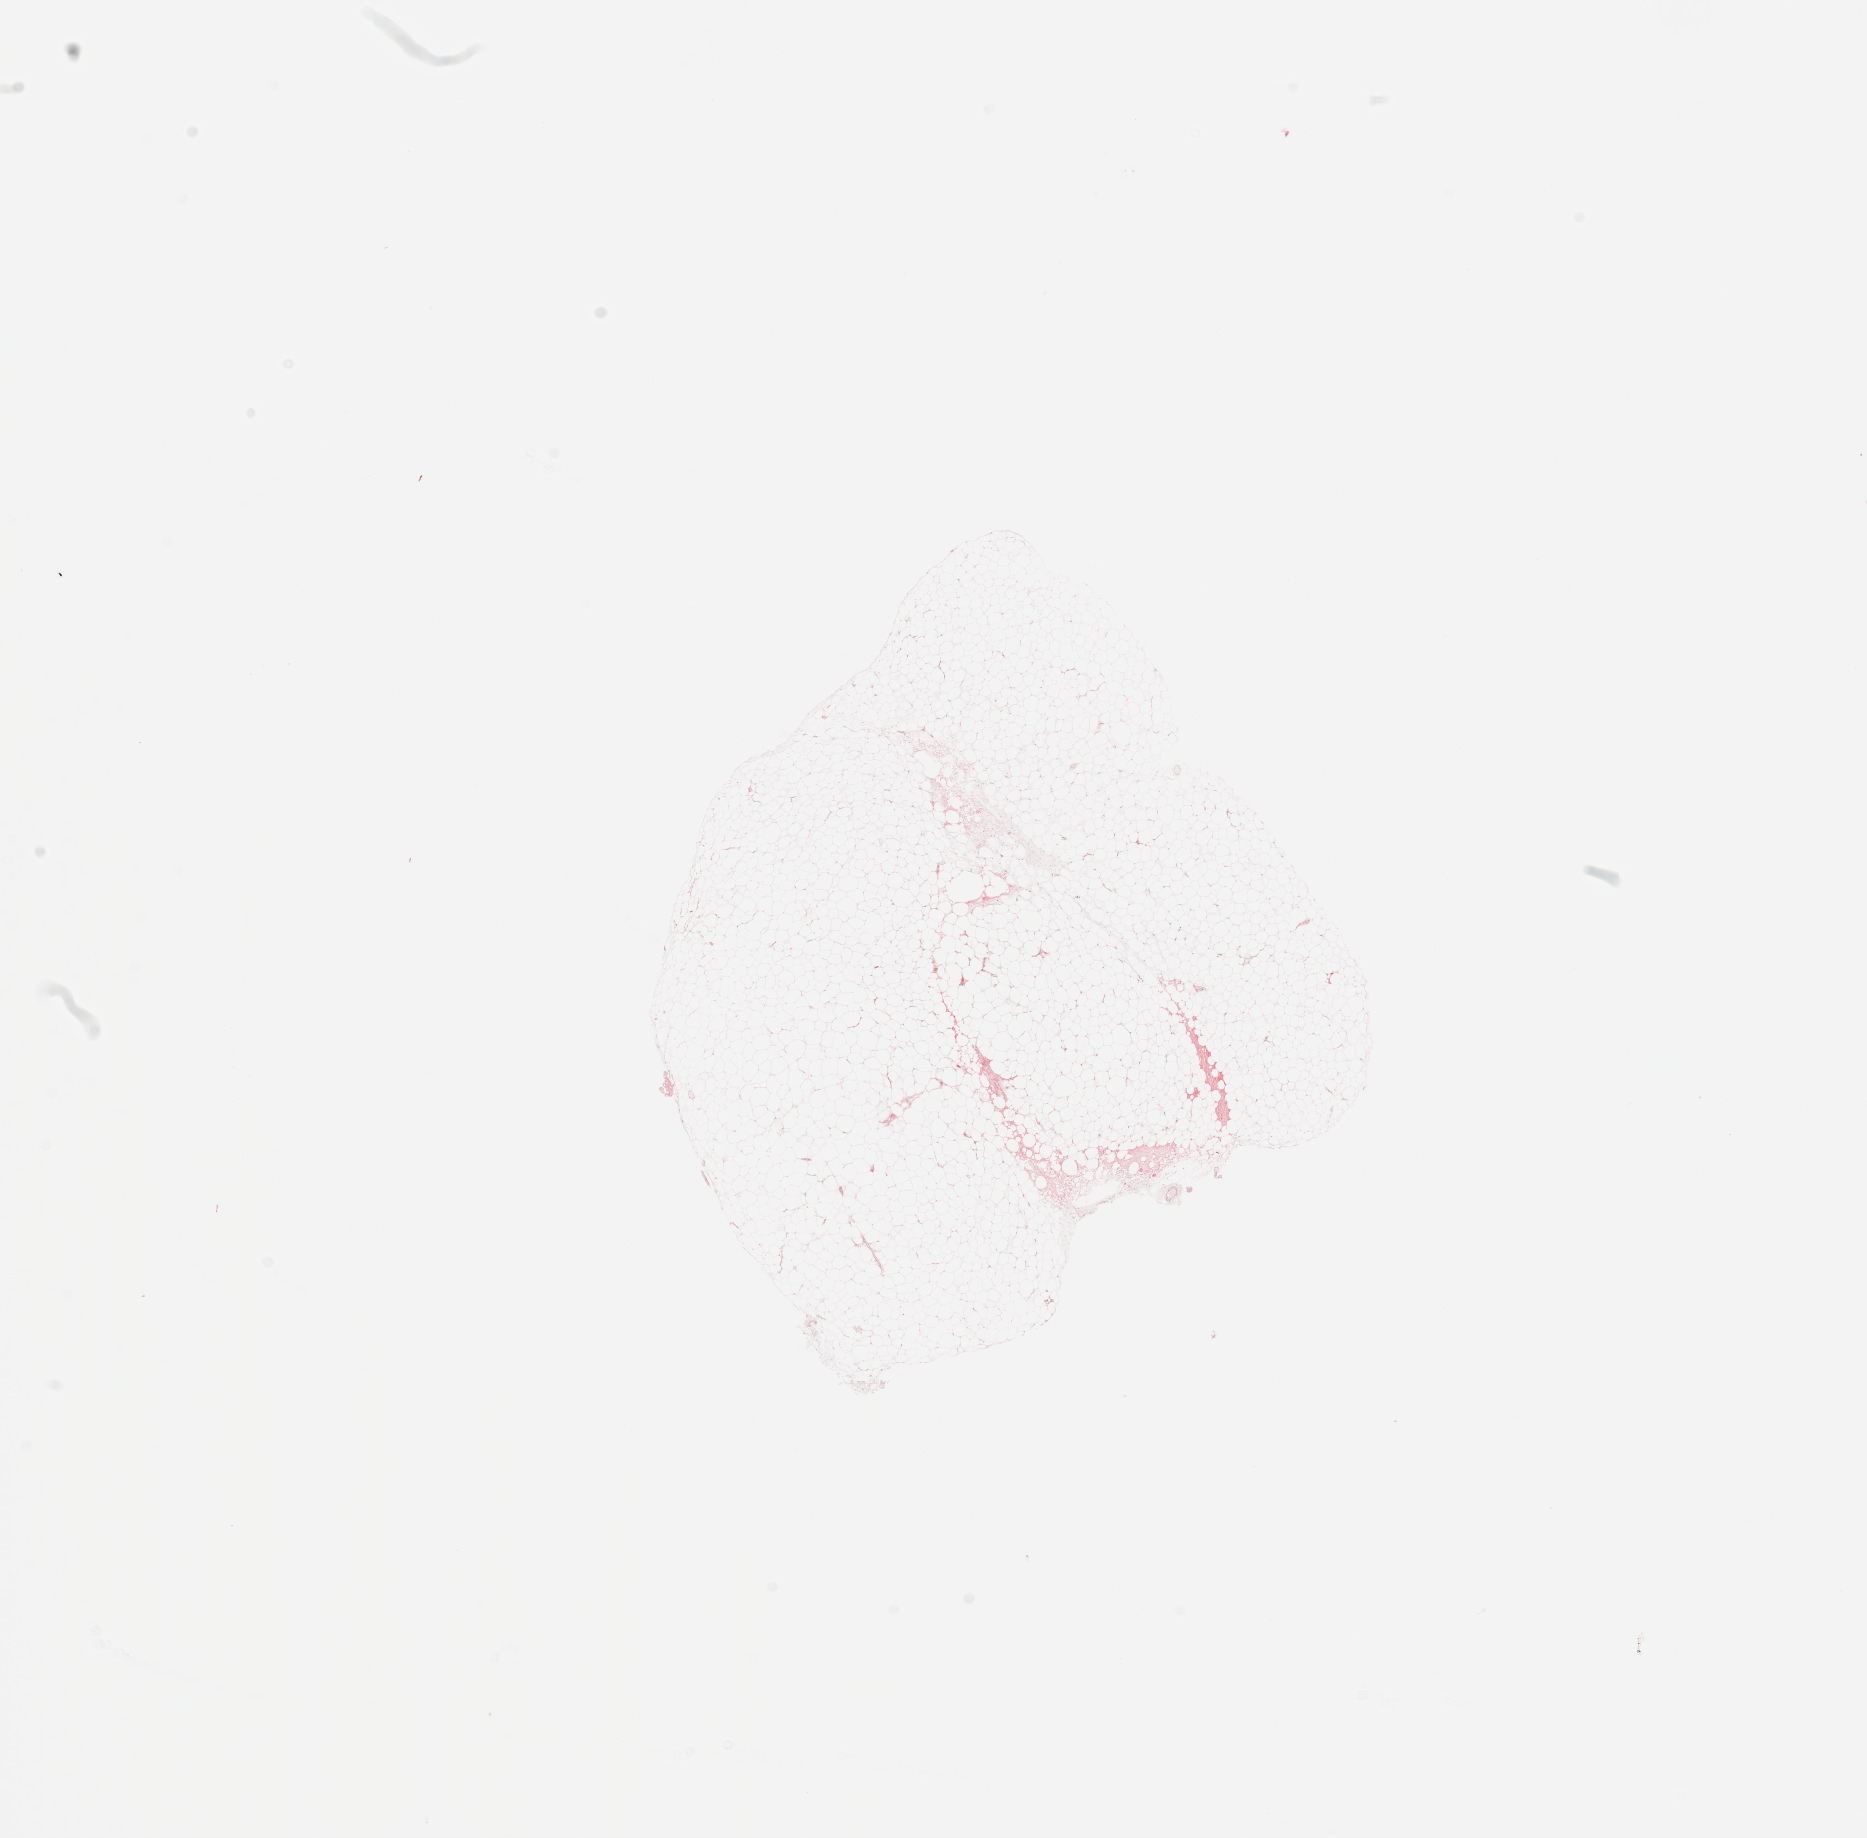
H&E-stained whole-slide image — low-resolution overview of the scanned area, about 14.8 x 14.5 mm (acquisition: 20x scan); kidney, normal (non-tumour) tissue. Patient: female, age 78 years.
- this section: normal (non-tumour) tissue from the same patient
- patient diagnosis: Renal cell carcinoma, NOS